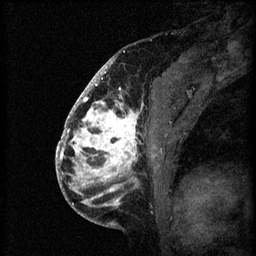
Breast MRI (dynamic contrast-enhanced), one sagittal slice; slice 35 of 60 in the series (ordered by position); 3 images stored at this slice position (order not interpretable as contrast timing); 1.5 T; TE 4.2 ms, TR 8.2 ms; 2 mm slice thickness; 256 × 256 image matrix. Female patient, age 41 years.
Outlined on this slice (semi-automatically segmented with operator editing):
- analysis volume of interest (the breast-tissue region the enhancement analysis was run in; not a lesion): bounding box (x1, y1, x2, y2) in pixels: (72, 108, 167, 205)
- tumour enhancement mask (voxels above the 70 % enhancement threshold inside the analysis volume of interest): (72, 108, 139, 205)